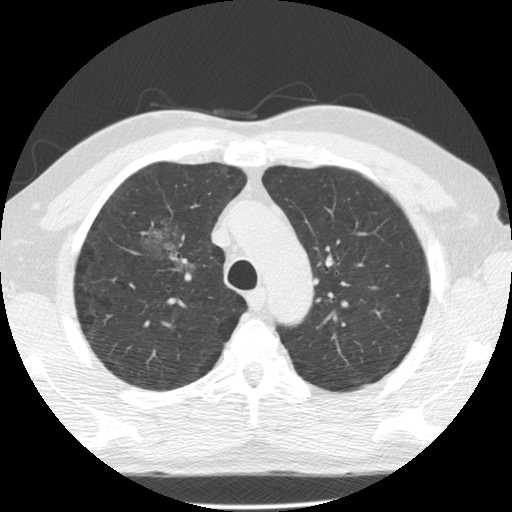
Low-dose screening chest CT, axial slice; second screening round (one year after baseline); lung window (W 1500 / L -600 HU); standard (soft-tissue) reconstruction kernel (STANDARD). Male, age 60 years at enrolment.
Lesion marked by an expert reader, bounding box (x1, y1, x2, y2) in pixels: (133, 214, 197, 275). Reader record for this screening exam (exam-level; its link to the box is not recorded): non-calcified nodule or mass ≥4 mm, right upper lobe, poorly defined margins, mixed attenuation, pre-existing on the prior screen: yes; interval growth: yes. Participant outcome: lung cancer diagnosed 562 days after this screen — papillary adenocarcinoma, NOS, right upper lobe, moderately differentiated (G2), stage IB (AJCC 6th edition), 32 mm at pathology.